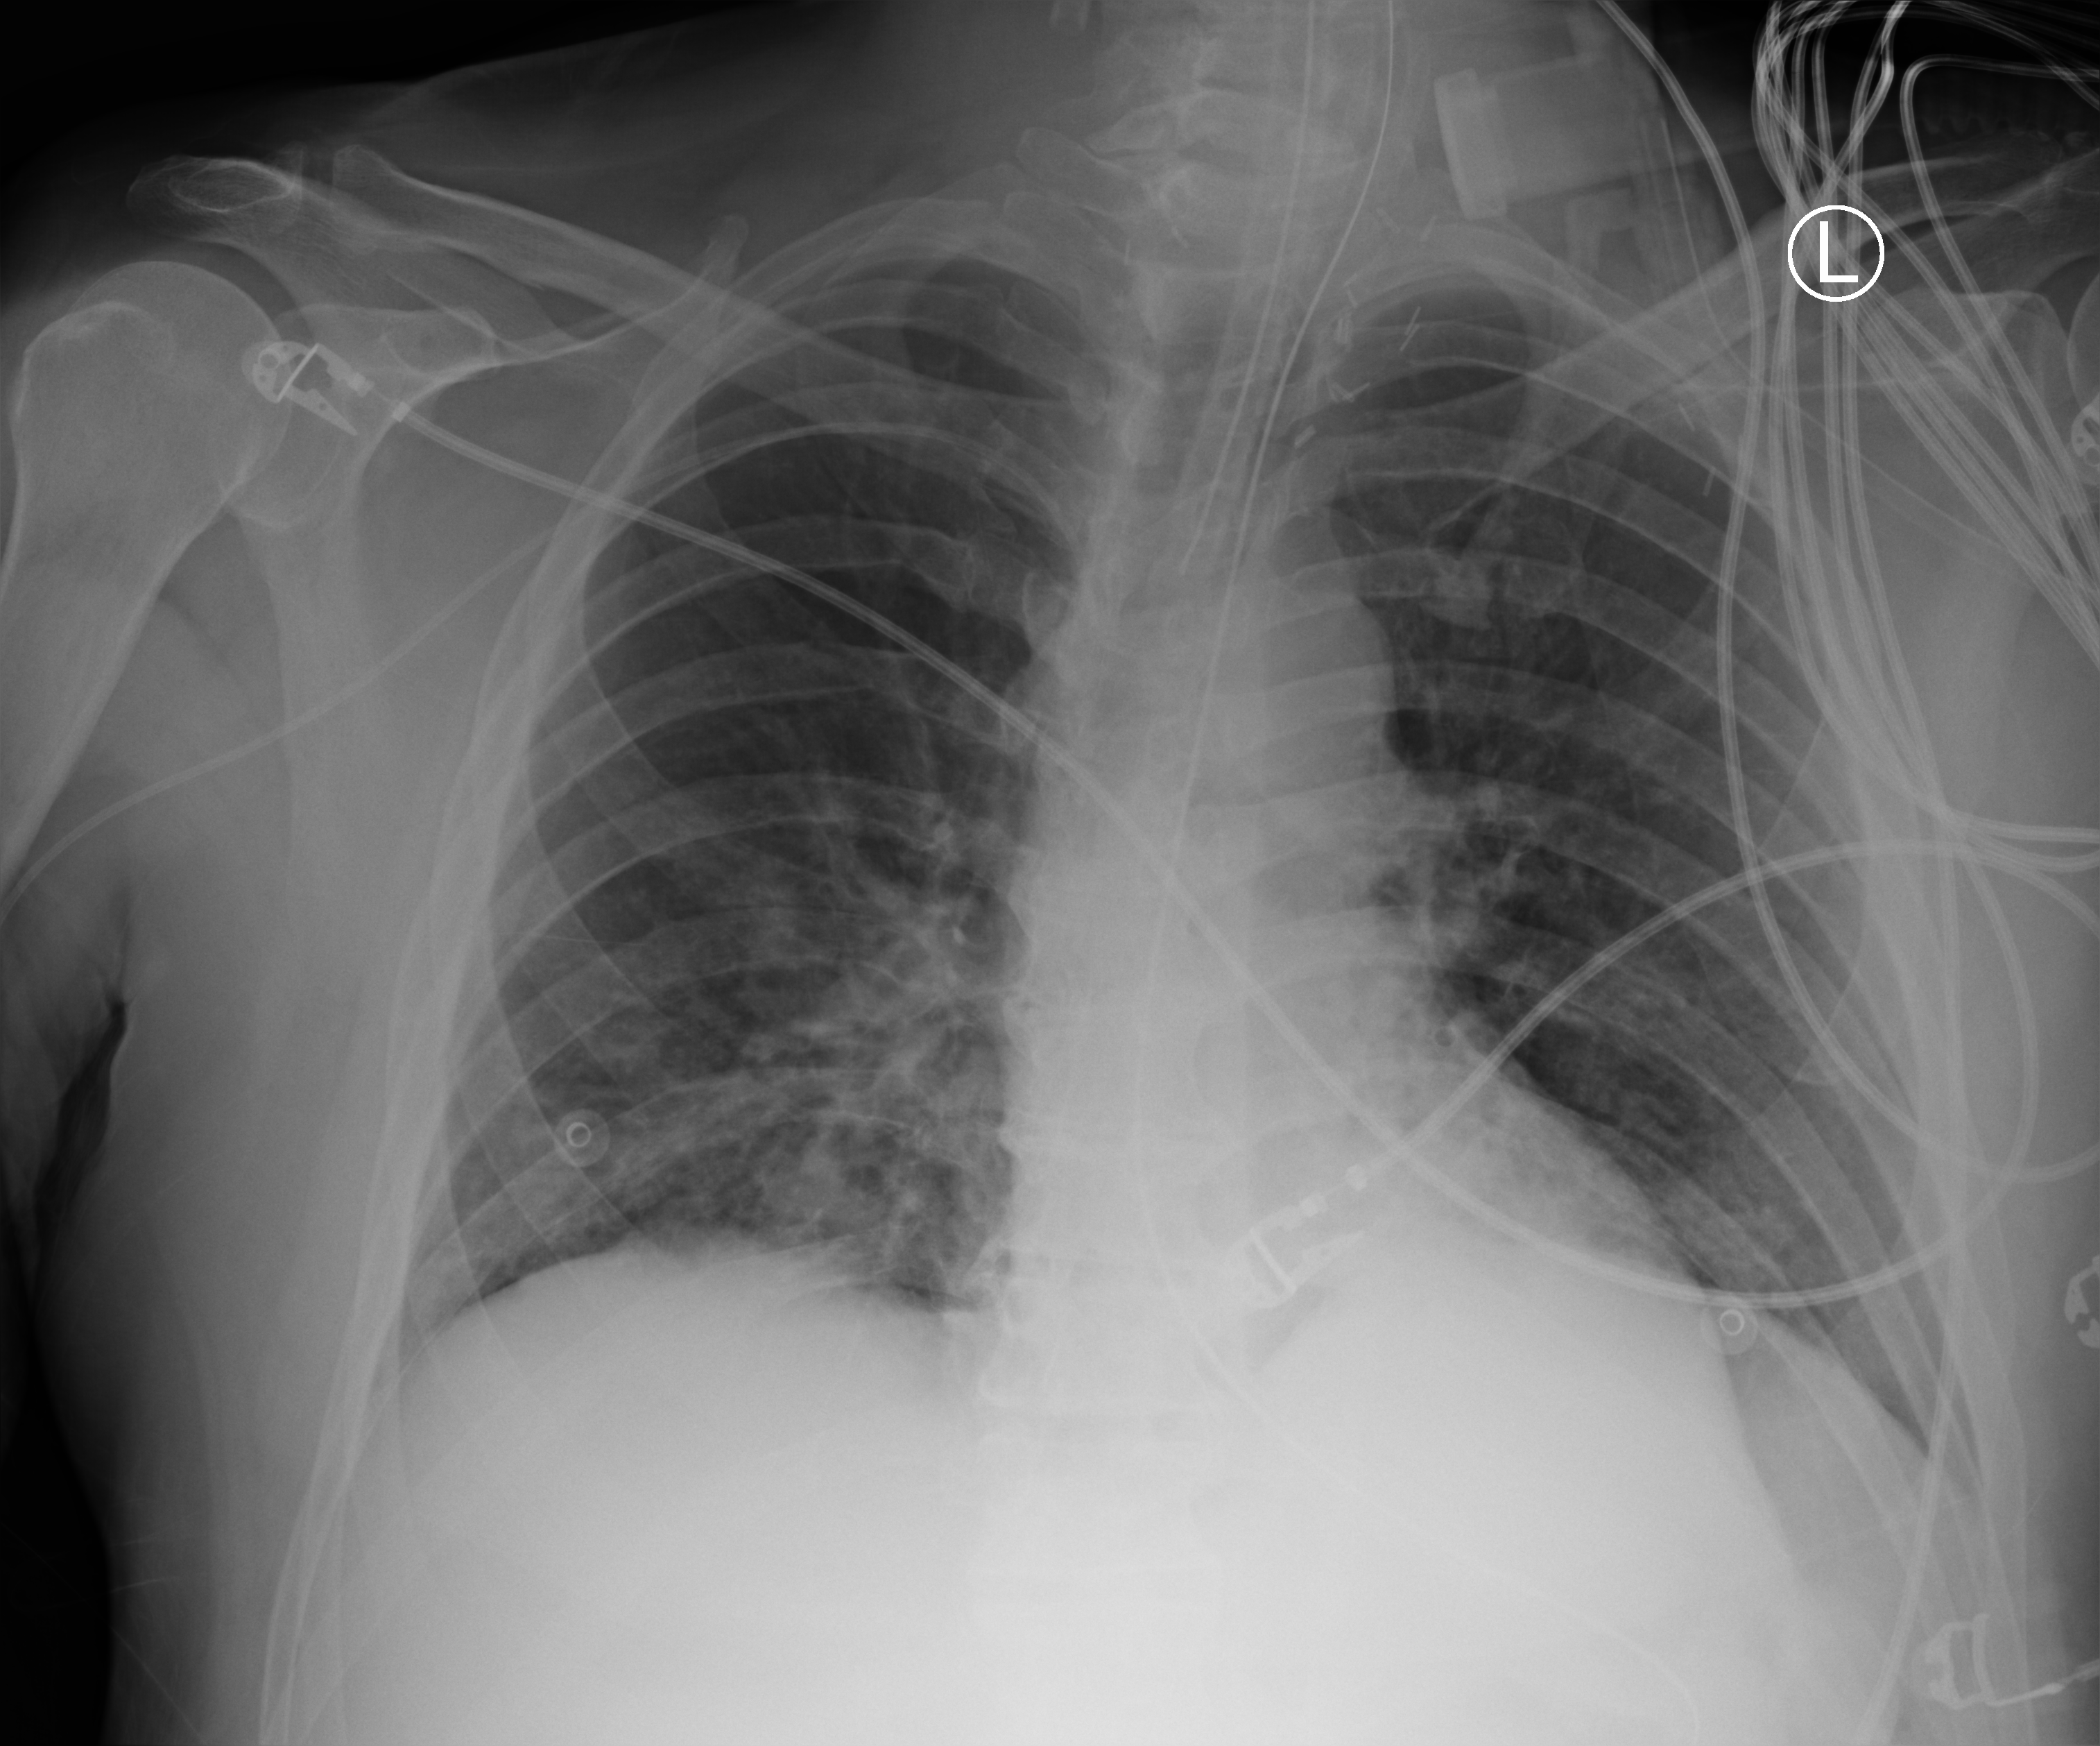
Portable chest radiograph, anteroposterior (AP) projection. Adult patient hospitalised with COVID-19, age 18–59 years.
Hospital-stay facts (about this admission, not read from this image; timing relative to this image not recorded): hypertension (admission record): no; length of hospital stay: 19 days; admitted to intensive care during this hospital stay: yes.